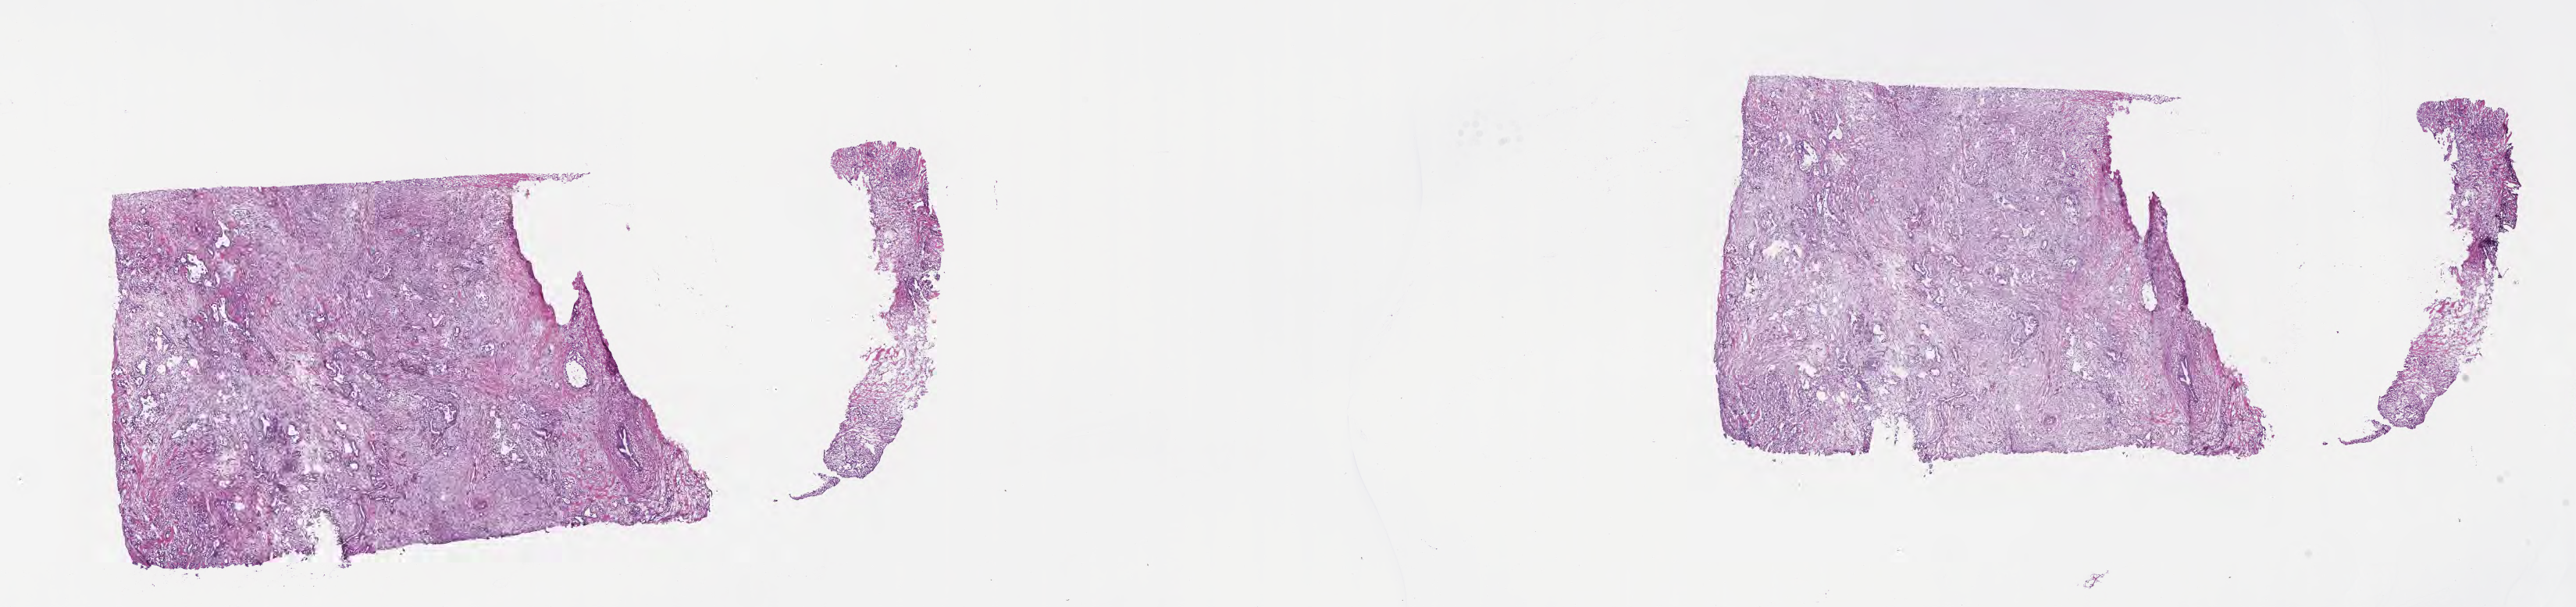
Digitized H&E-stained section, shown as a low-resolution overview of the whole scanned area (about 26.7 x 6.3 mm). Frozen section. Specimen: primary tumor. Site: tail of pancreas. Female, age 68 years at initial diagnosis. Composition of this section per pathologist review: tumor cells 98%, tumor nuclei 50%, stromal cells 0%, necrosis 2%, normal cells 0%. Inflammatory infiltration, as recorded: lymphocyte infiltration 0%, monocyte infiltration 0%, neutrophil infiltration 0%.
Diagnosis: Infiltrating duct carcinoma, NOS.